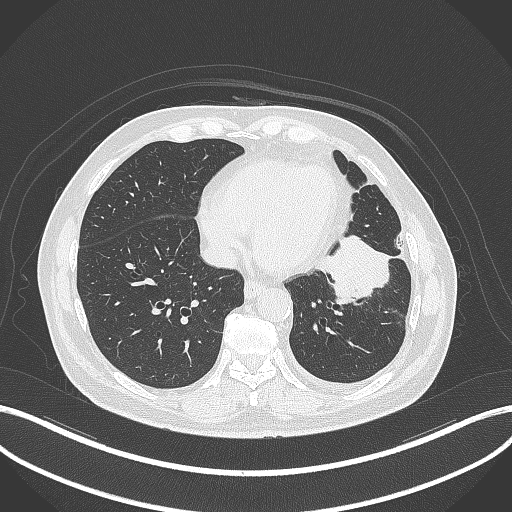
Chest CT, one axial slice; position 116 of 230 along the scan axis; 120 kVp; lung window (W 1500 / L -600 HU); 512 × 512 image matrix. Patient: male, 68 years. Case-level facts recorded for this patient, not image findings: clinical TNM (as recorded): T2b N0 M0.
Structures marked on this image (rectangle marked by the reading radiologist):
- lung tumour (recorded histology: squamous cell carcinoma): bounding box (x1, y1, x2, y2) in pixels: (315, 229, 396, 310)